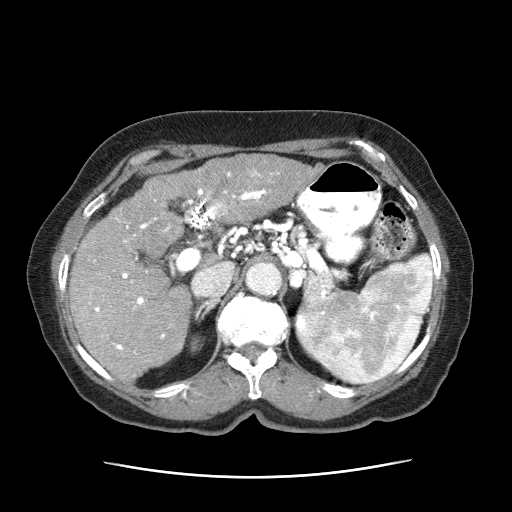
Contrast-enhanced abdominal CT (liver protocol), one axial slice. Reconstruction kernel STANDARD. Soft-tissue window (W 400 / L 40 HU). 2.5 mm slice thickness. 512 × 512 image matrix. Patient: female, 79 years. Case-level facts recorded for this patient, not image findings: diagnosis: hepatocellular carcinoma (patient treated with transarterial chemoembolisation; whether this scan precedes or follows treatment is not stated here); TNM stage (as recorded): Stage-II; Child-Pugh class: B; tumour differentiation: well differentiated; tumour nodularity: multinodular.
Structures marked on this image (semi-automatic segmentation, software-assisted and operator-edited):
- abdominal aorta: bounding box [x1, y1, x2, y2] px = [246, 262, 282, 296]
- liver parenchyma outside the tumour (the mass and vessels are separate outlines, so this box may not span the whole liver): [69, 176, 234, 383]
- mass: [155, 154, 311, 224]
- liver vessels: [88, 172, 280, 355]